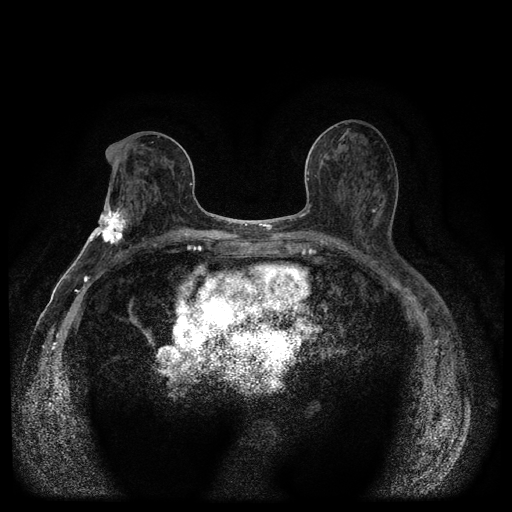
Breast MRI (dynamic contrast-enhanced, multi-phase), one axial slice. Position 53 of 116 along the scan axis. Dynamic contrast-enhanced series, time point 2 of 5 at this slice position (early post-contrast). 1.5 T. TE 2.7 ms, TR 5.4 ms. 2 mm slice thickness. 512 × 512 image matrix. Patient: female, 75 years.
Outlined on this slice (semi-automatically segmented with operator editing):
- breast lesion (labelled 'tumour' in the annotation; benign lesions carry a separate 'benign' label): bounding box (x1, y1, x2, y2) in pixels: (89, 200, 128, 247)